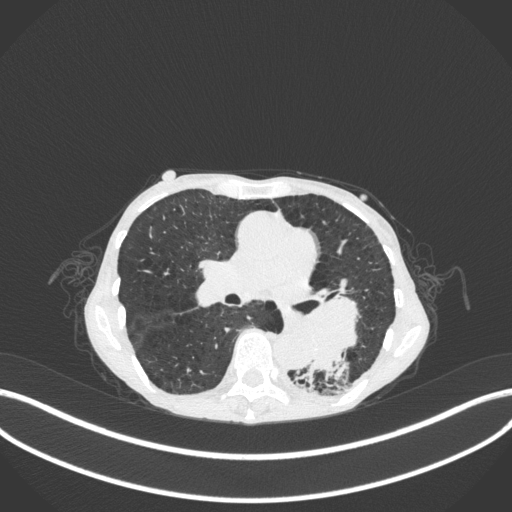
Chest CT, one axial slice; reconstruction kernel B31f; lung window (W 1500 / L -600 HU); 512 × 512 image matrix, field of view 400 × 400 mm. Female patient, age 70 years. From the clinical record (not read from this slice): clinical TNM (as recorded): T3 N0 M0.
Annotated regions visible in this slice (bounding box drawn by a radiologist):
- lung tumour (recorded histology: small cell carcinoma): bounding box <271,293,367,371> (left, top, right, bottom; pixels)